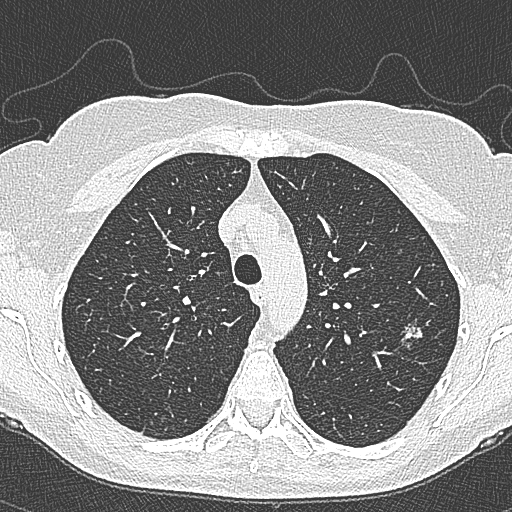
Low-dose screening chest CT, axial slice. Second annual screen. Lung window (W 1500 / L -600 HU). Lung (sharp) reconstruction kernel (B80f). Slice 84 of 350 in the series. Female, age 65 years at enrolment. Current smoker at enrolment.
Lesion marked by an expert reader, bounding box (x1, y1, x2, y2) in pixels: (396, 311, 444, 360). The screening reader recorded 4 non-calcified nodules or masses ≥4 mm on this exam (left upper lobe, left upper lobe, left upper lobe, right lower lobe); which of them this box marks is not recorded. Lung cancer was diagnosed 54 days after this screen: bronchiolo-alveolar carcinoma, non-mucinous, left upper lobe, stage IA (AJCC 6th edition), 10 mm at pathology.